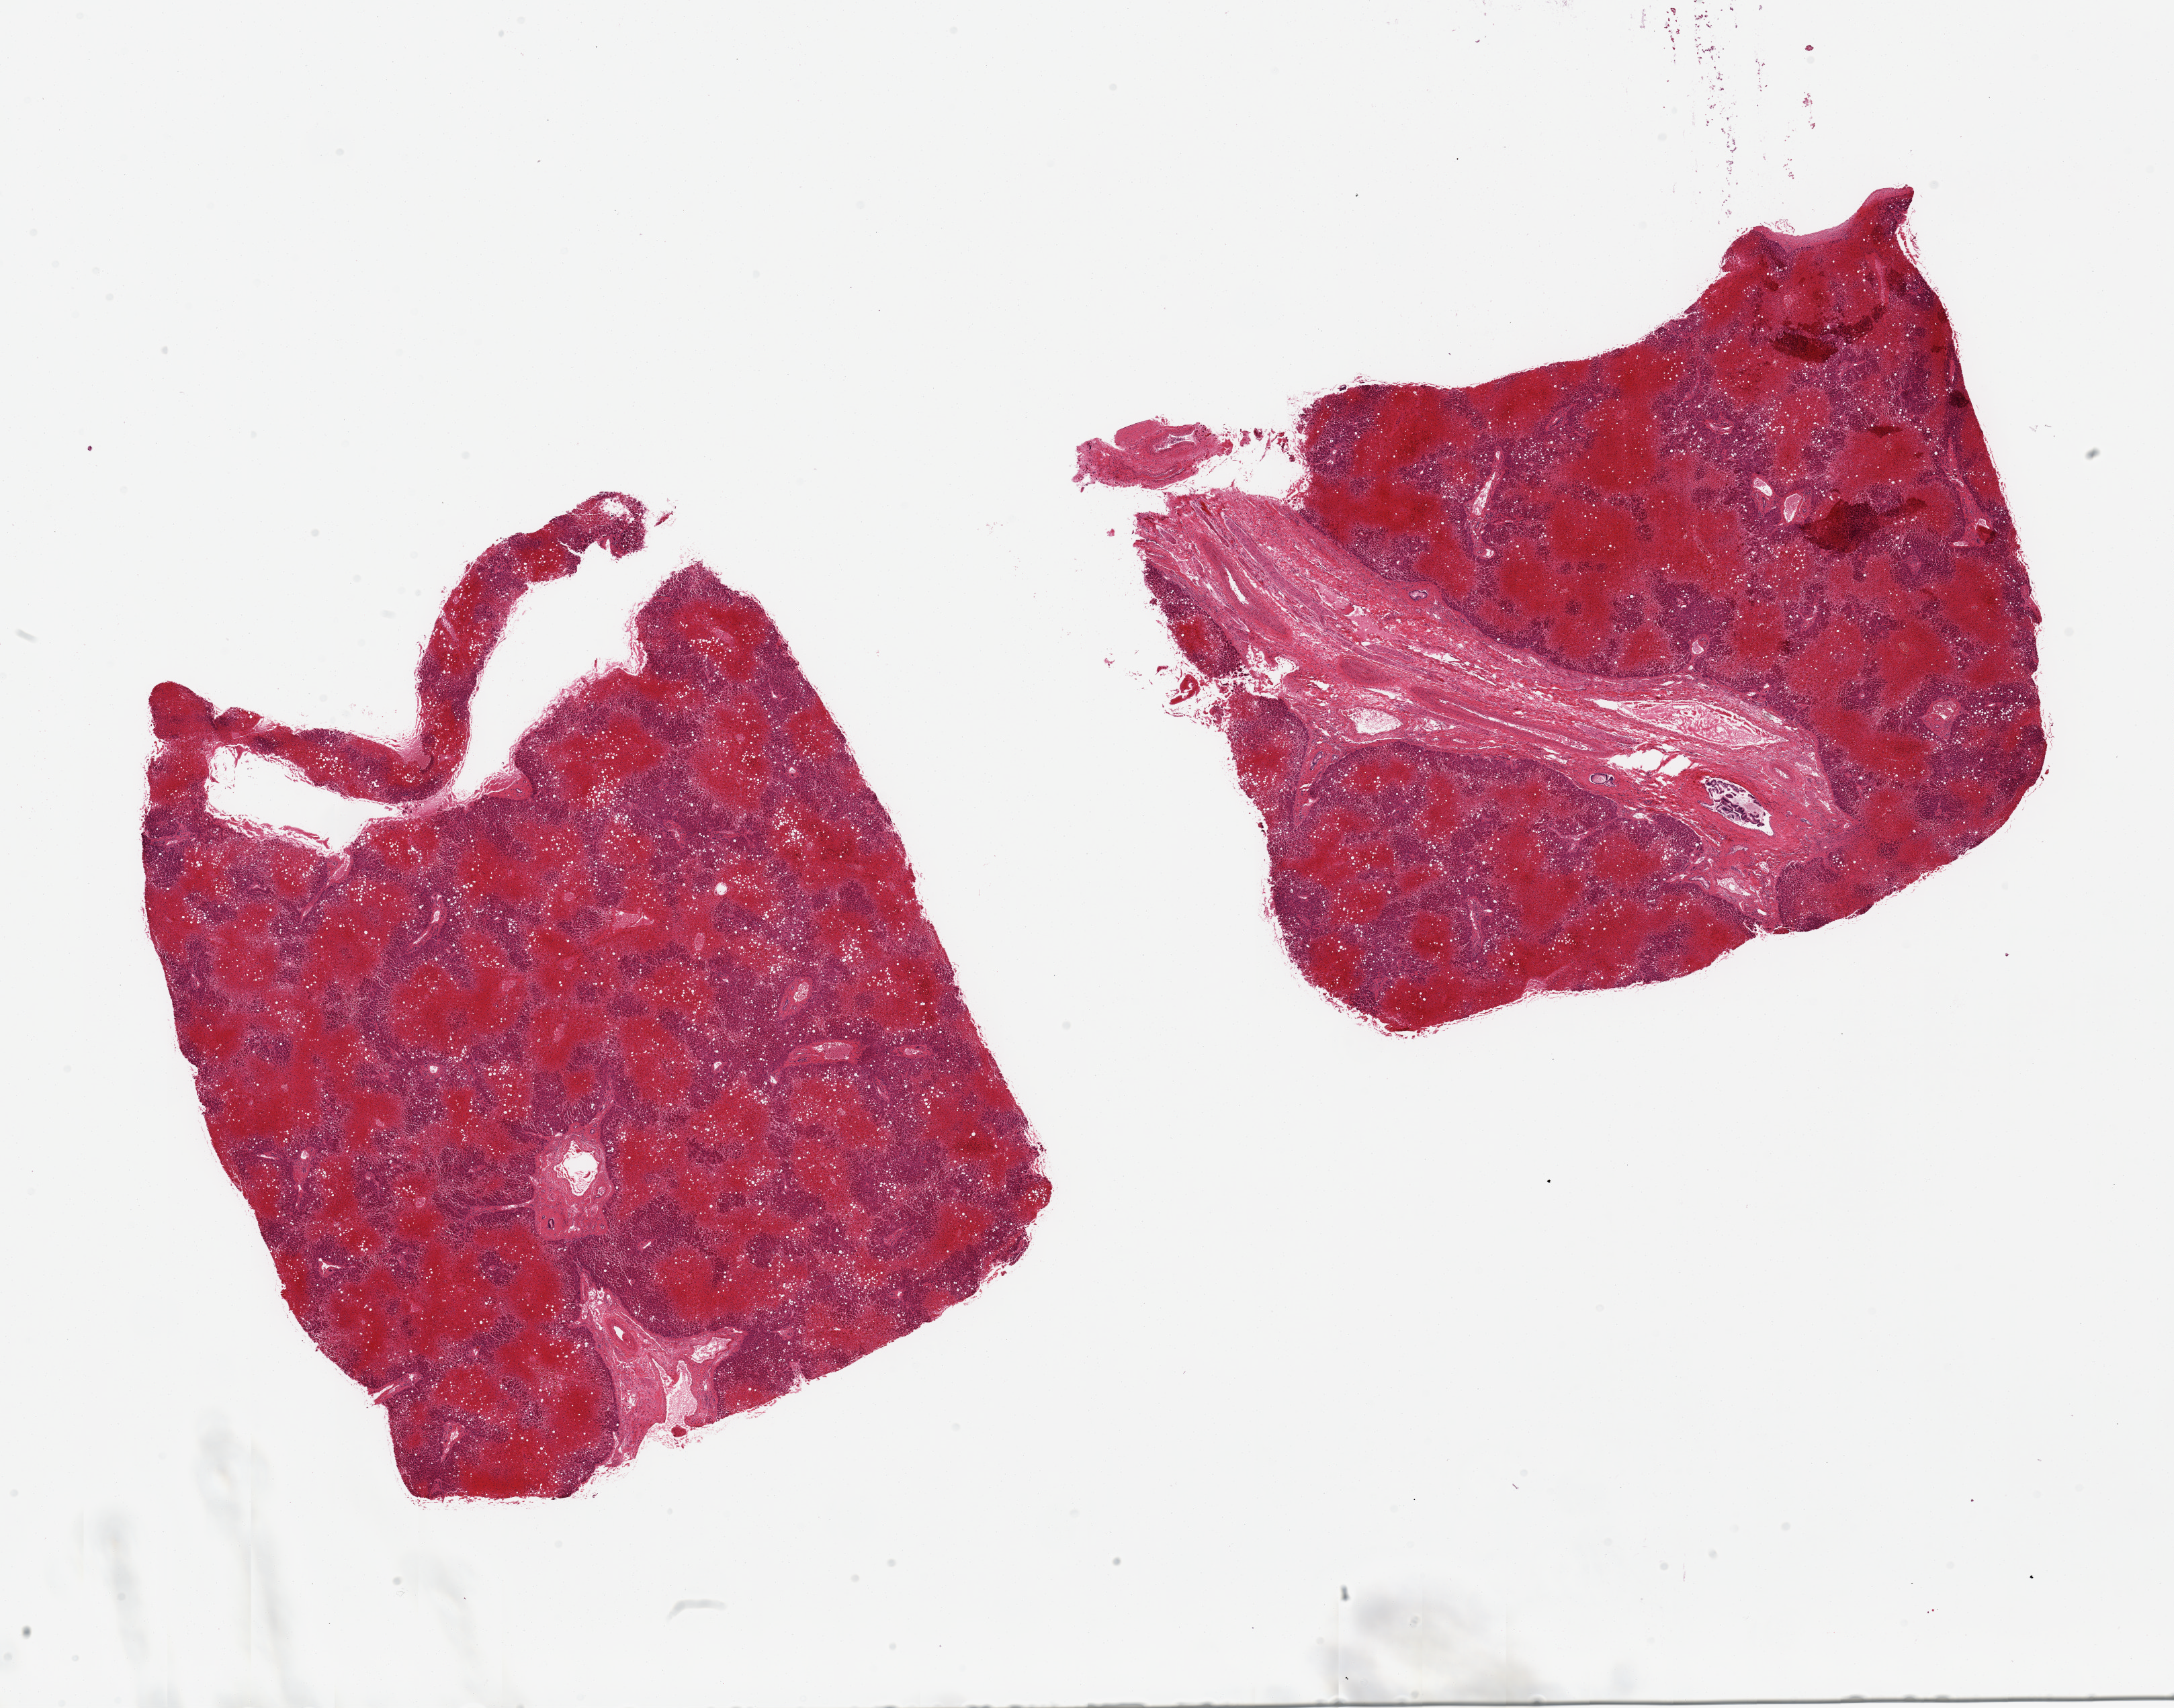
Whole-slide image, H&E stain, whole scanned area (about 25.6 x 20.1 mm, acquisition: 20x scan) shown as a low-resolution overview; PAXgene-fixed, paraffin-embedded tissue; sampled site (target tissue): liver; tissue donor sample. Donor sex: male.
- pathologist's review note for this sample: 2 pieces massive central hemorrhagic necrosis/submassive hepatic necrosis, ~30% mascrovesicular steatosis